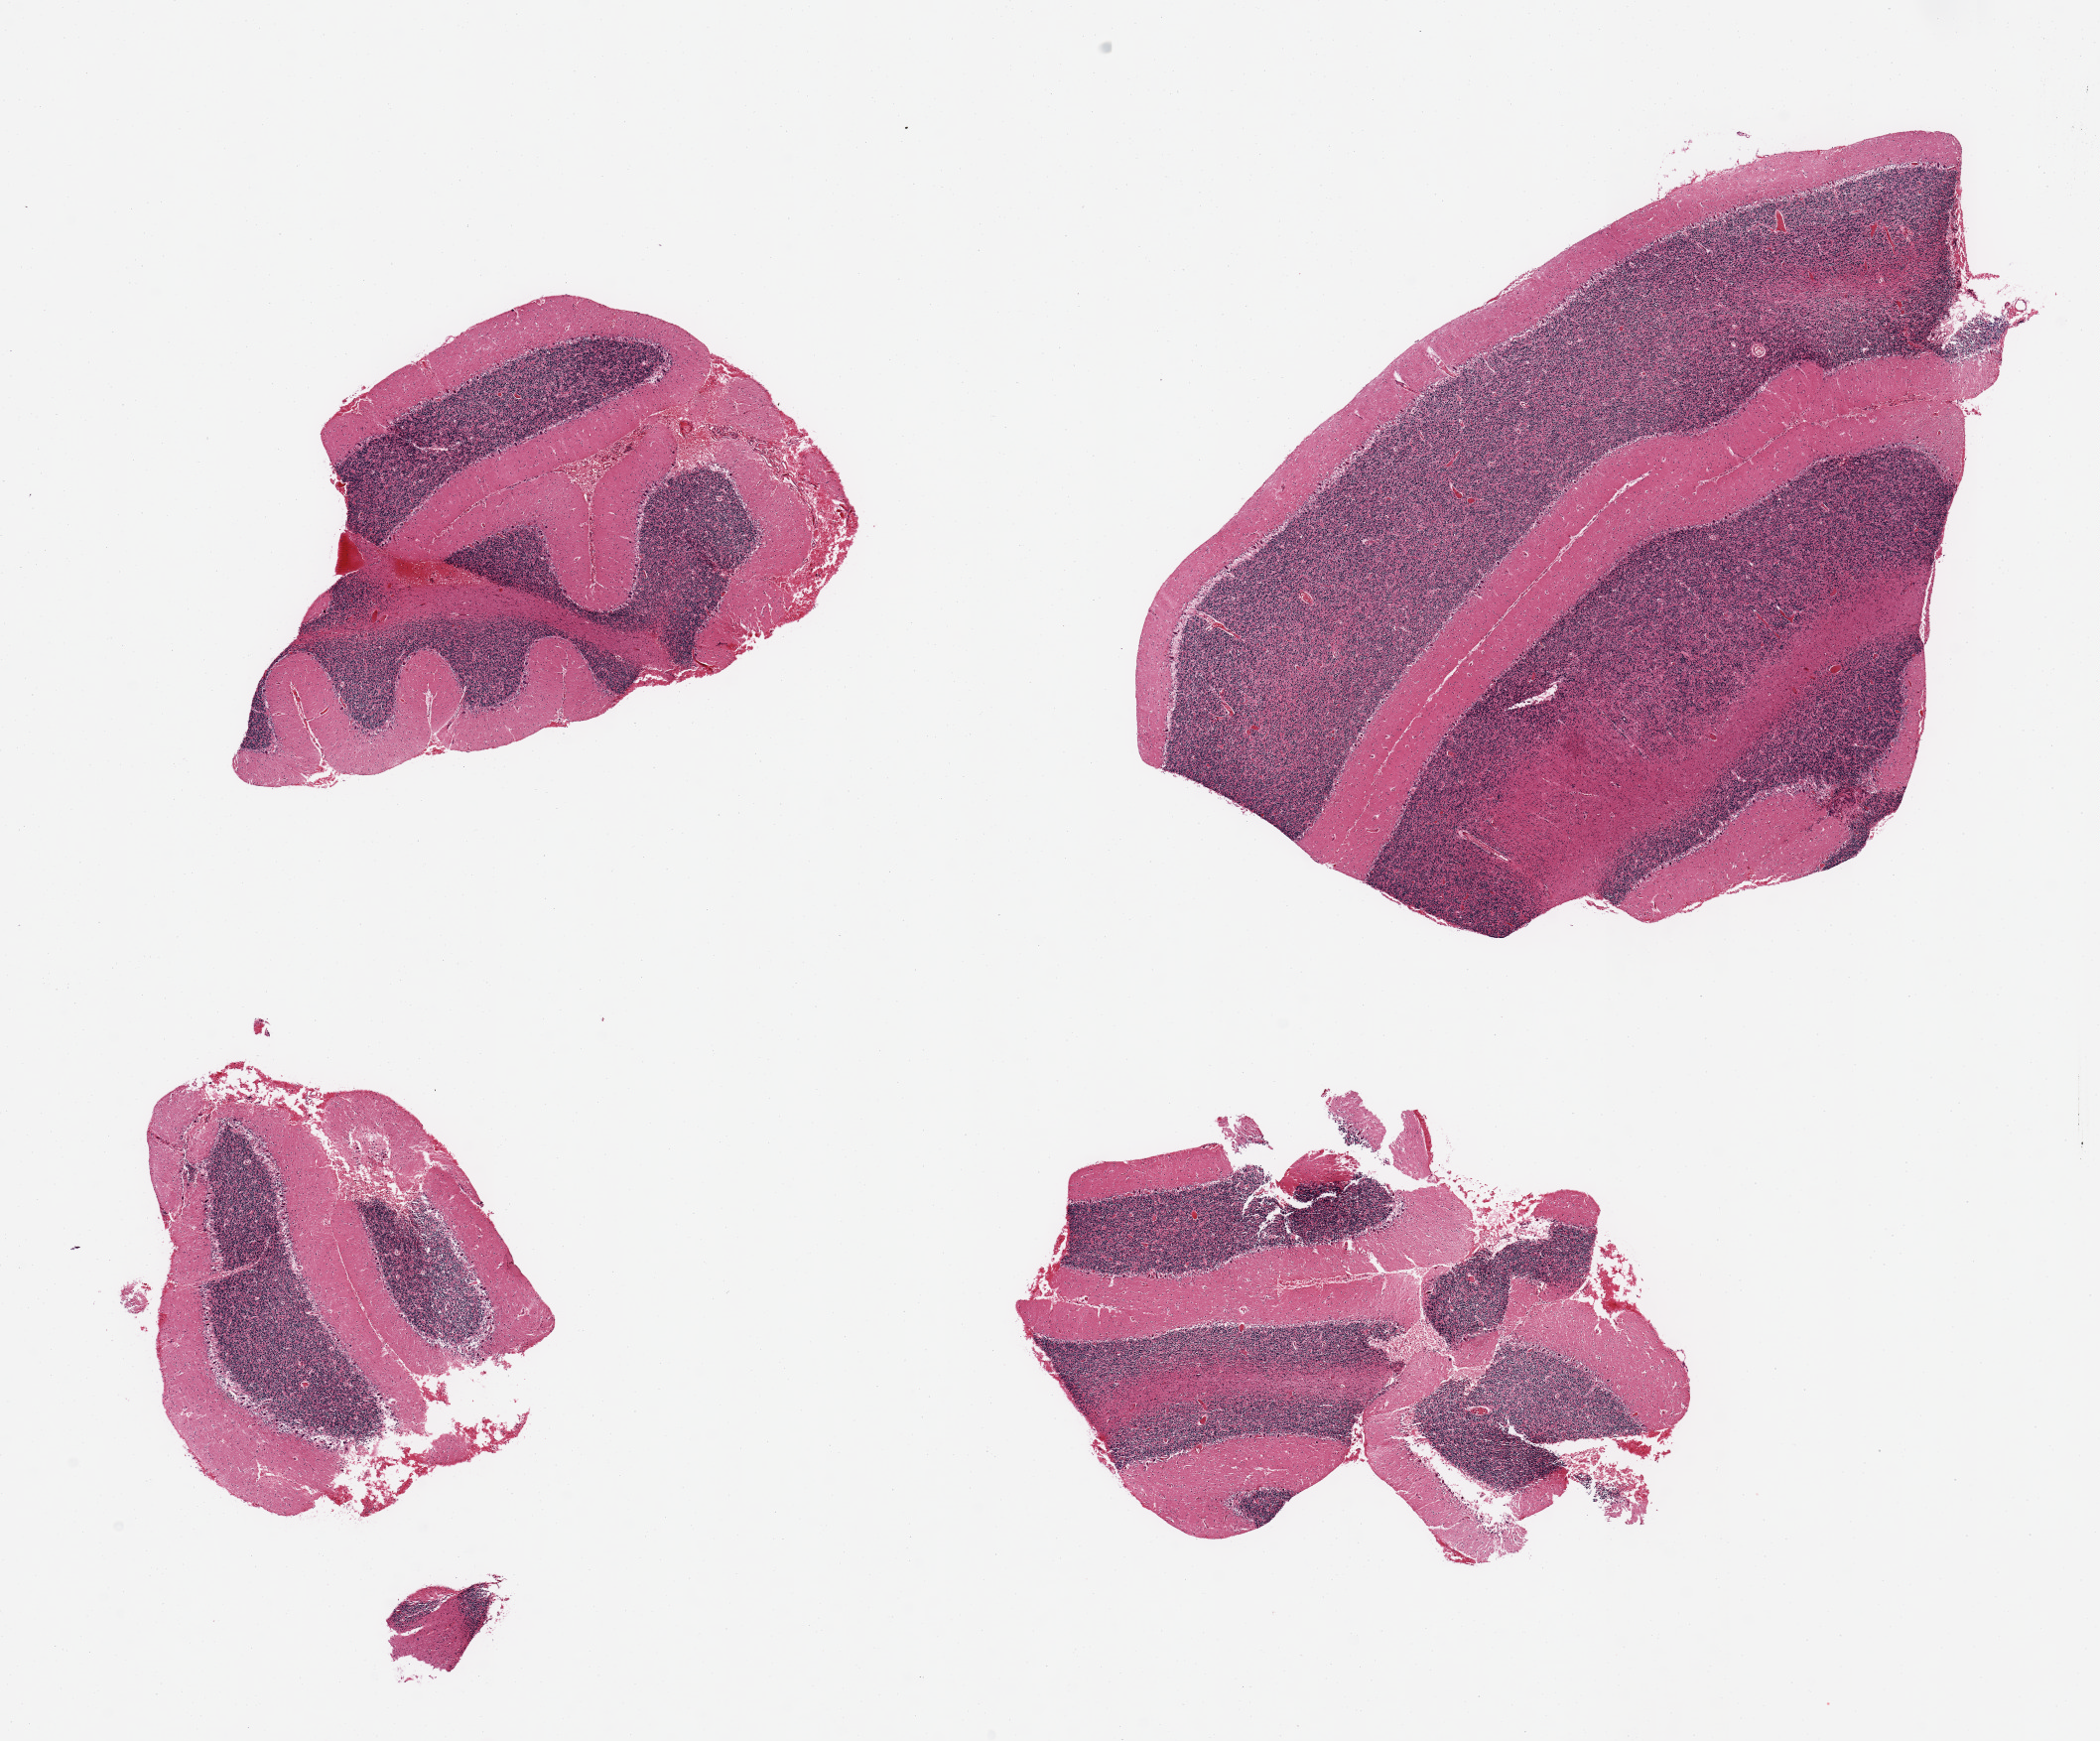
Digitized H&E-stained section, brightfield, a low-resolution overview of the entire scanned area, about 16.7 x 13.9 mm; PAXgene-fixed paraffin-embedded (PFPE) section; sampled site (target tissue): cerebellum; tissue donor sample. Female donor.
- review note (as recorded): 4 pieces